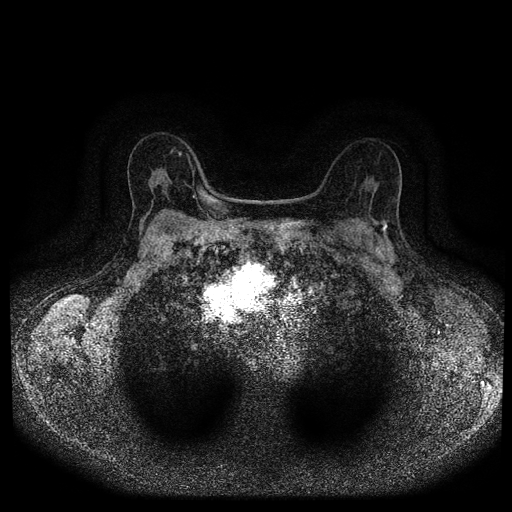
Breast MRI (dynamic contrast-enhanced, multi-phase), one axial slice. Slice 63 of 116 in the series (ordered by position). Dynamic contrast-enhanced series, time point 2 of 5 at this slice position (early post-contrast). 1.5 T. TE 2.7 ms, TR 5.4 ms. 512 × 512 image matrix, field of view 330 × 330 mm. Patient: female, 63 years.
Structures marked on this image (semi-automatically segmented with operator editing):
- breast lesion (labelled 'tumour' in the annotation; benign lesions carry a separate 'benign' label): bounding box <378,218,392,238> (left, top, right, bottom; pixels)